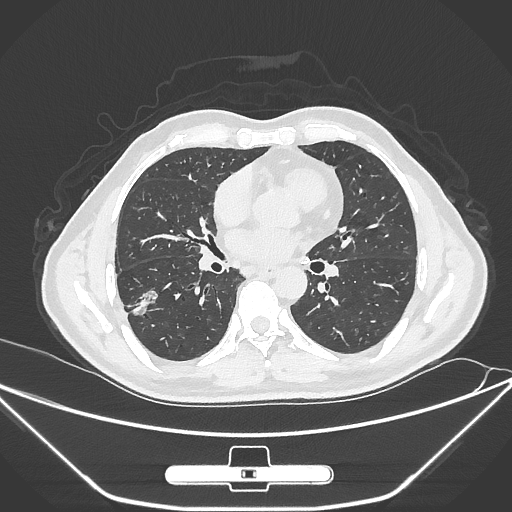
Chest CT, one axial slice; slice 143 of 310 in the series (ordered by position); reconstruction kernel IMR1,SharpPlus; 120 kVp; lung window (W 1500 / L -600 HU); 512 × 512 image matrix. Patient: male, 71 years. Case-level facts recorded for this patient, not image findings: clinical TNM (as recorded): T1c N0 M0; histopathological grade: G2.
Annotated regions visible in this slice (bounding box drawn by a radiologist):
- lung tumour (recorded histology: adenocarcinoma): bounding box <125,277,163,327> (left, top, right, bottom; pixels)